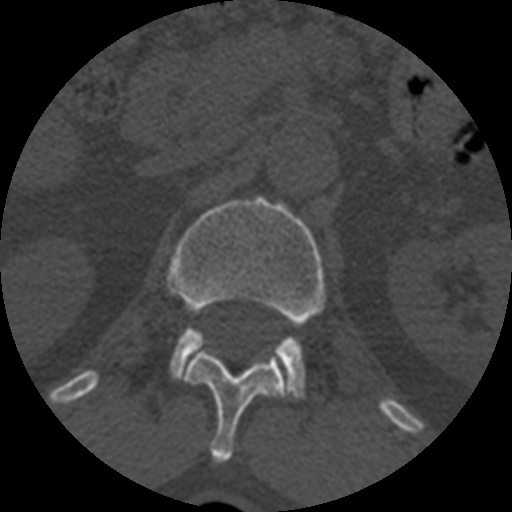
CT including the spine, one axial slice; position 372 of 399 along the scan axis; reconstruction kernel STANDARD; 120 kVp; bone window (W 1800 / L 400 HU); 512 × 512 image matrix. Patient age 71 years. Case-level facts recorded for this patient, not image findings: primary cancer: prostate.
Structures marked on this image (semi-automatically segmented with operator editing):
- L1 vertebra: bounding box <168,198,325,401> (left, top, right, bottom; pixels)
- T12 vertebra: <183,349,289,462>